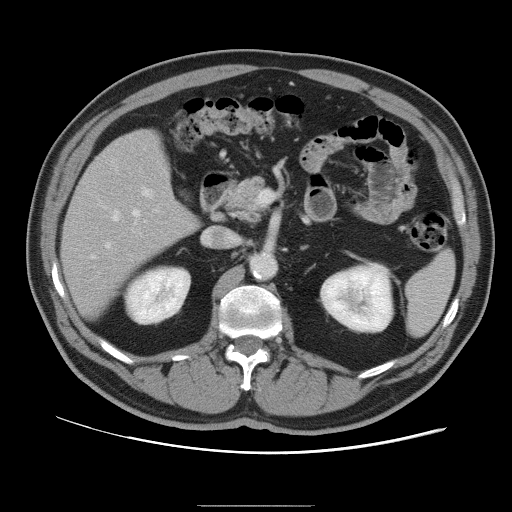
Contrast-enhanced abdominal CT, one axial slice. Slice 50 of 105 in the series (ordered by position). 120 kVp. Intravenous contrast given. Soft-tissue window (W 400 / L 40 HU). 5 mm slice thickness. 512 × 512 image matrix. Male patient, age 64 years. Case-level facts recorded for this patient, not image findings: diagnosis: colorectal cancer liver metastases, imaged before liver resection; multiple liver metastases: yes; largest metastasis: 3 cm.
Outlined on this slice (outlined manually by an expert reader):
- hepatic veins: bounding box (x1, y1, x2, y2) in pixels: (92, 209, 140, 259)
- liver: (63, 130, 198, 316)
- planned liver remnant (the part of the liver to remain after resection): (63, 130, 198, 316)
- portal vein (with intrahepatic branches): (105, 187, 154, 248)